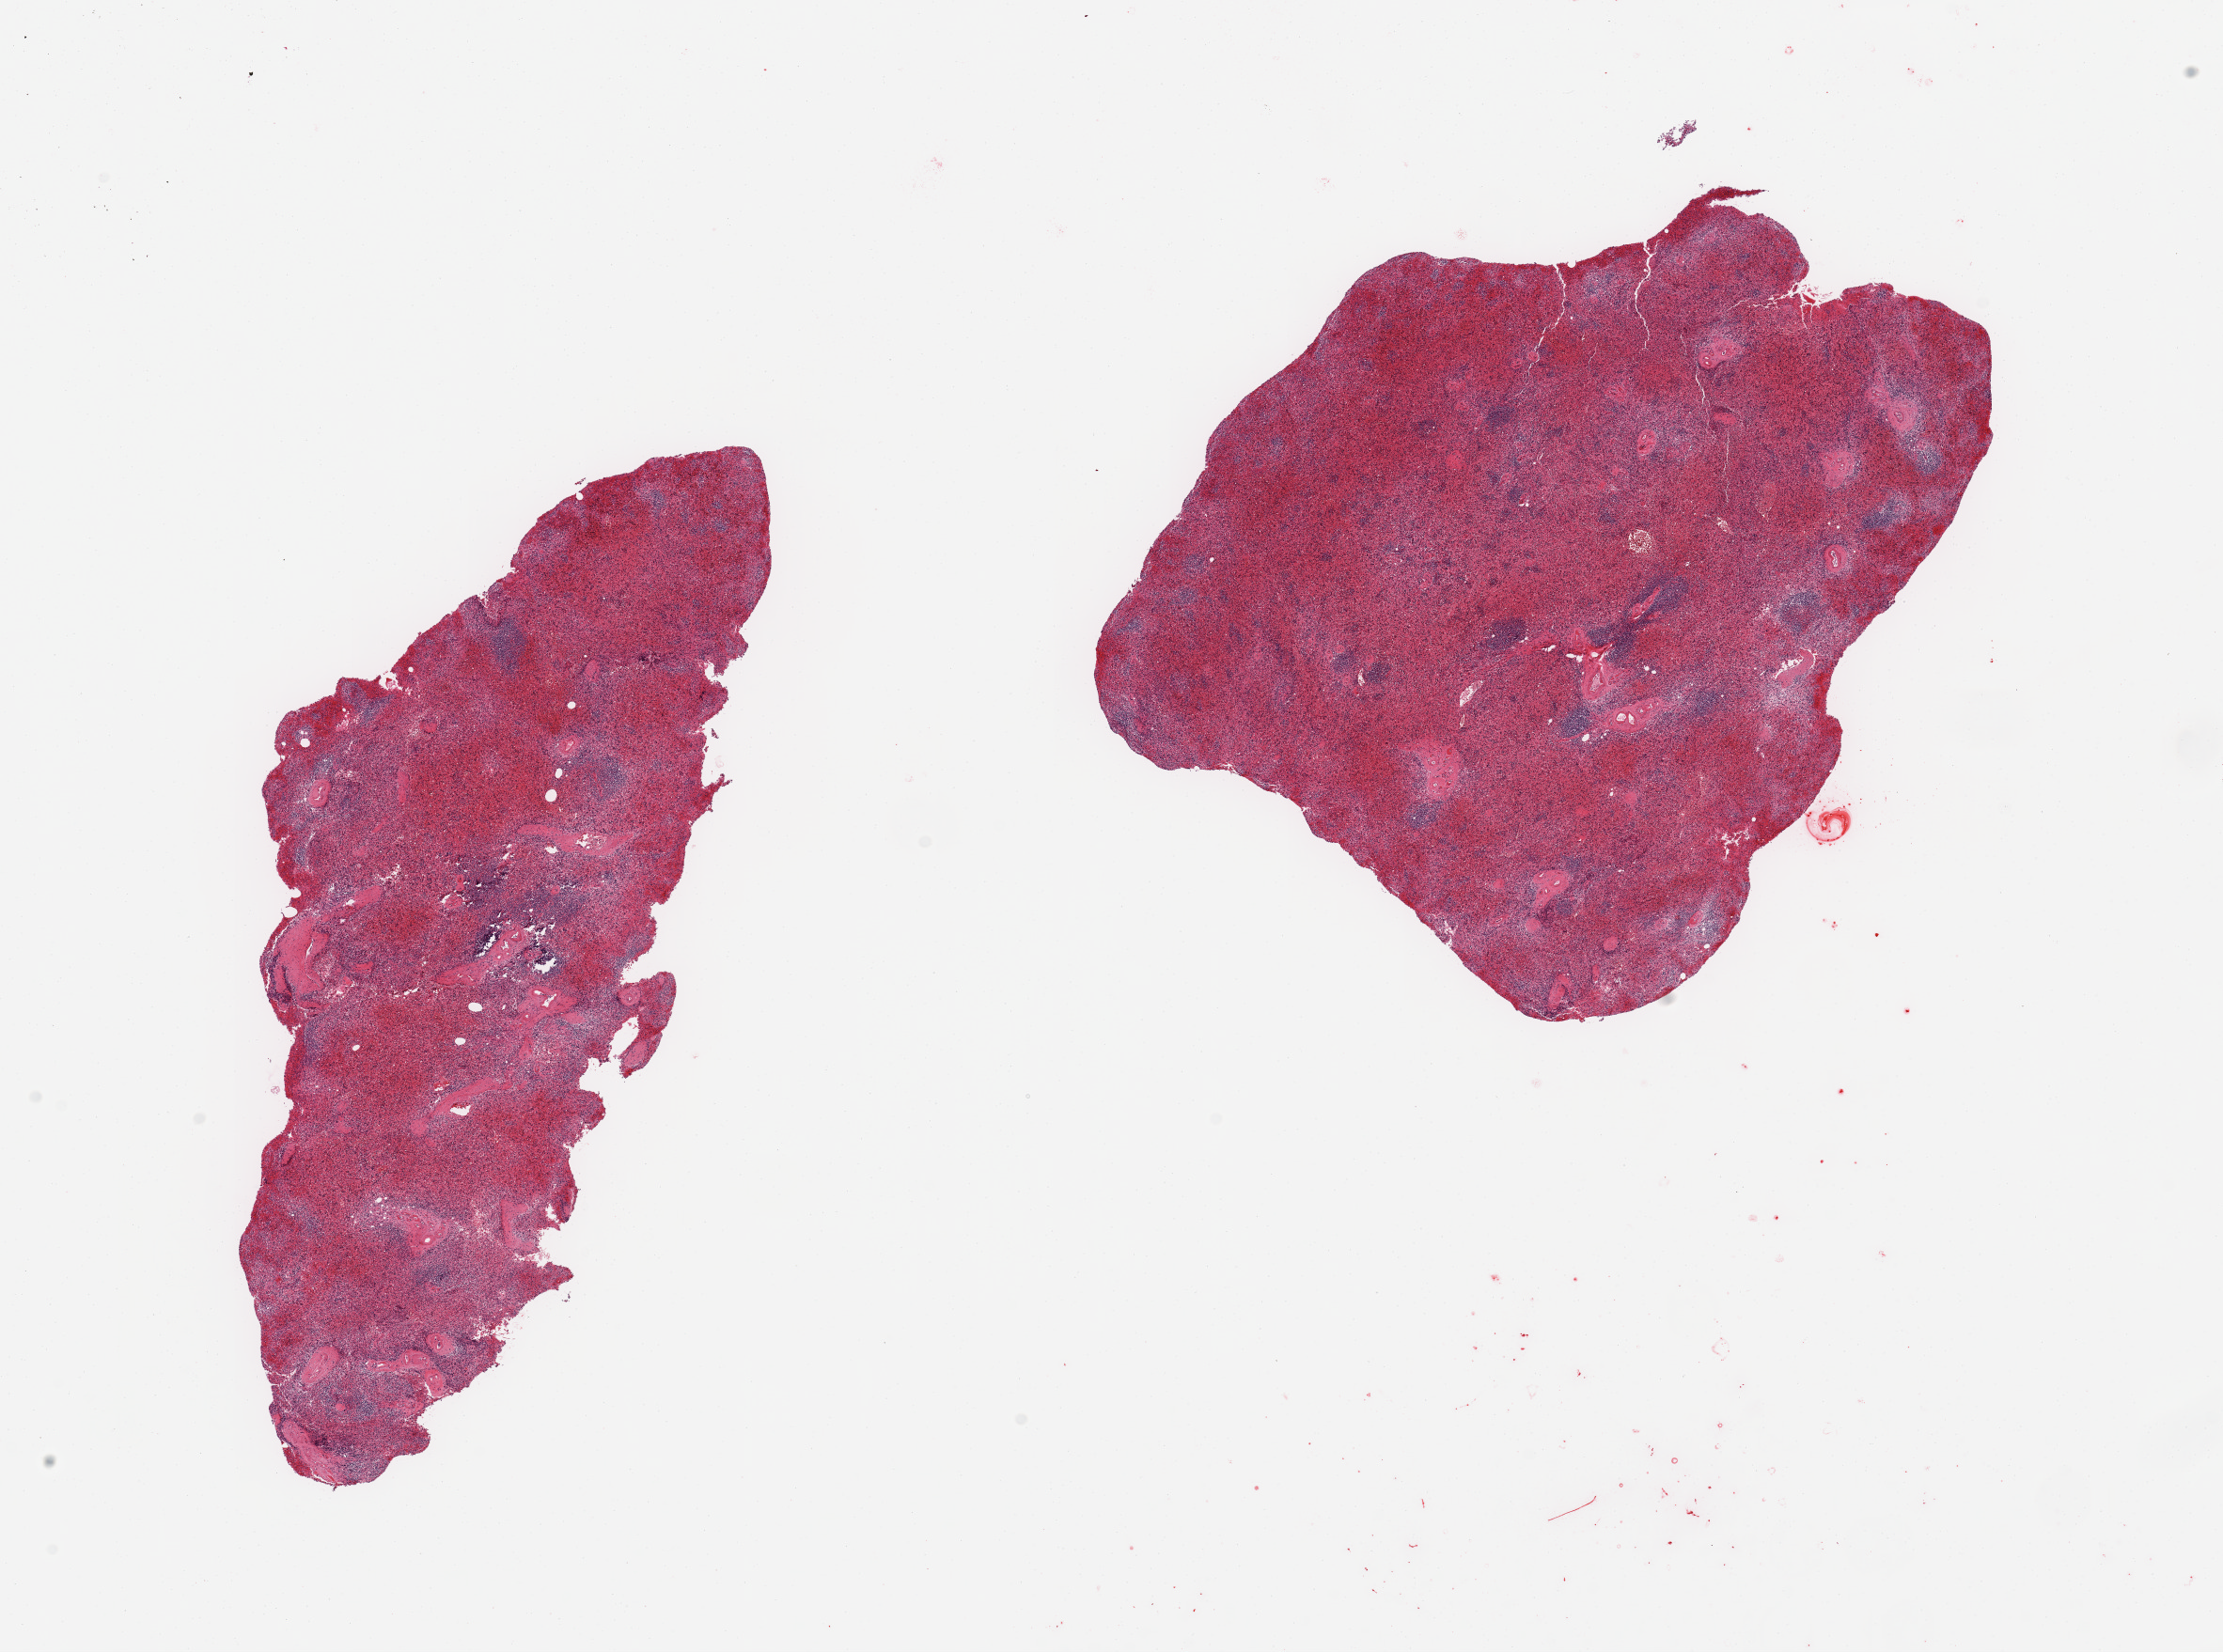
H&E whole-slide image, whole scanned area (about 18.7 x 13.9 mm) shown as a low-resolution overview, PAXgene-fixed paraffin-embedded (PFPE) section, target tissue: spleen, donor tissue sample. Donor: male.
Pathologist's review note for this sample: 2 pieces; moderately congested.